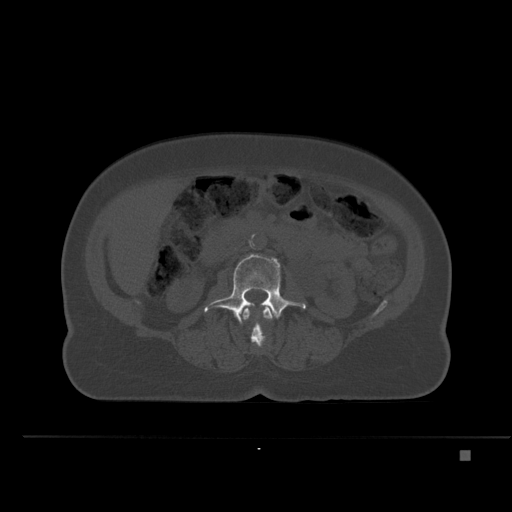
CT including the spine, one axial slice; slice 202 of 477 in the series (ordered by position); bone window (W 1800 / L 400 HU); 1.5 mm slice thickness; 512 × 512 image matrix, field of view 422 × 422 mm. Patient: female, 74 years. Case-level facts recorded for this patient, not image findings: primary cancer: colon.
Annotated regions visible in this slice (semi-automatic segmentation, software-assisted and operator-edited):
- L2 vertebra: bounding box (x1, y1, x2, y2) in pixels: (243, 305, 273, 347)
- L3 vertebra: (204, 253, 306, 324)